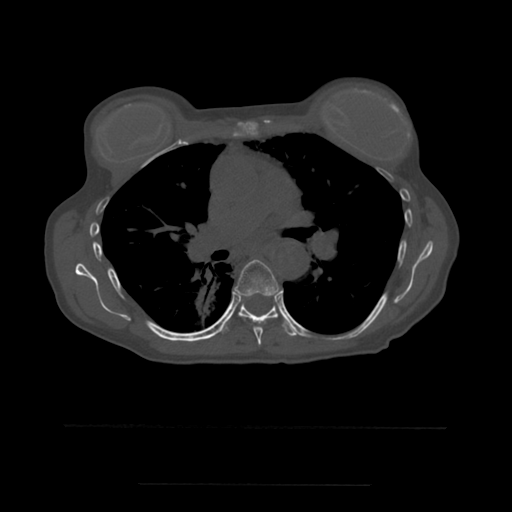
CT including the spine, one axial slice; slice 367 of 544 in the series (ordered by position); bone window (W 1800 / L 400 HU); 512 × 512 image matrix, field of view 350 × 350 mm. Patient age 58 years. Case-level facts recorded for this patient, not image findings: primary cancer: lung.
Annotated regions visible in this slice (semi-automatic segmentation, software-assisted and operator-edited):
- T6 vertebra: box from (x=233, y=260) to (x=279, y=346) px
- T7 vertebra: (x=220, y=295)–(x=297, y=338)